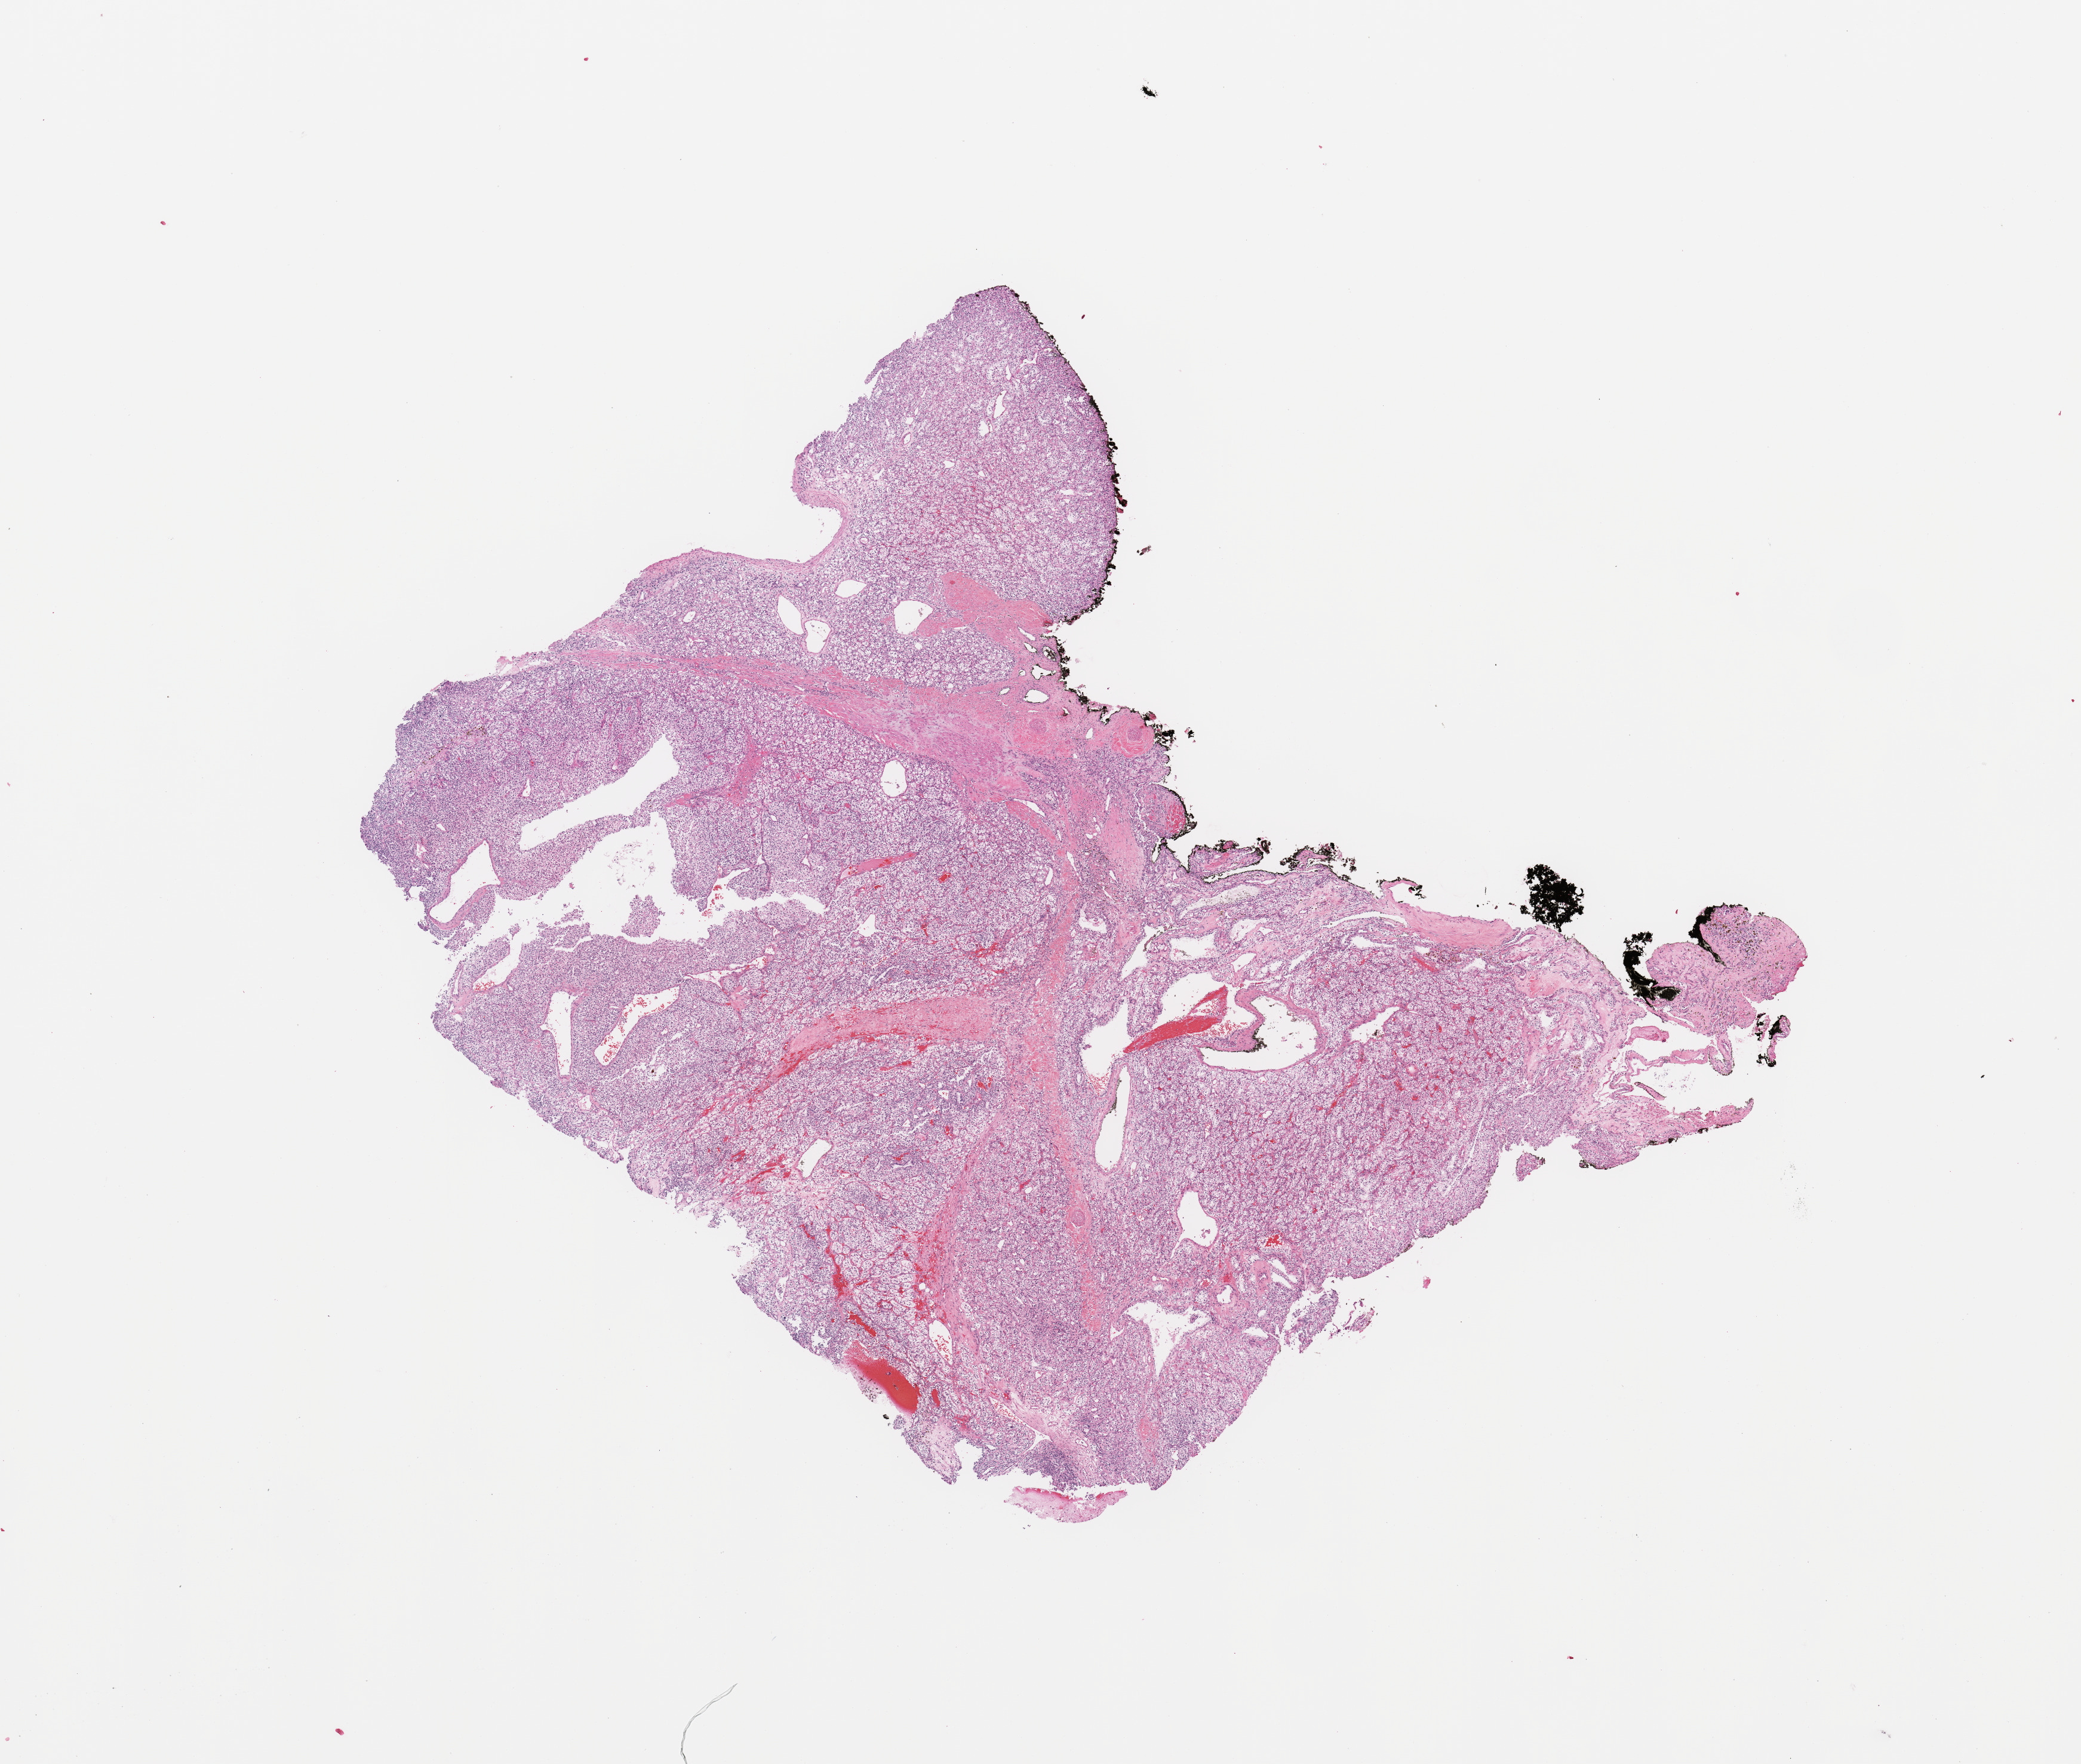
Whole-slide histology image, H&E — low-resolution overview of the scanned area, about 13.8 x 11.7 mm, tumour tissue sample, sampled site: kidney. 51-year-old female patient. Histologic grade: G3 (poorly differentiated). Slide review estimates, as recorded: tumour nuclei 90%, necrosis 2%.
AJCC pathologic stage: II. Diagnosis: Renal cell carcinoma, NOS.